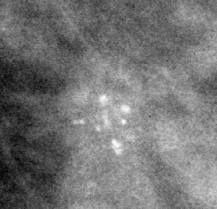
Region of interest cut from a scanned film mammogram (one marked finding); right breast; CC view; BI-RADS breast density category 3 (scale 1–4).
Finding: calcifications, morphology pleomorphic, distribution clustered; BI-RADS assessment category 4; pathology result (as recorded, not read from the image): malignant.